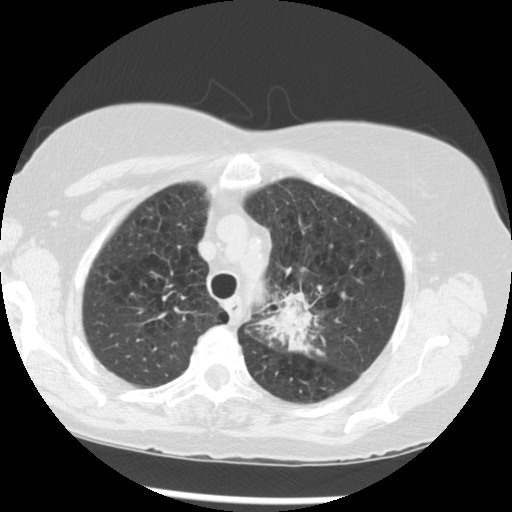
Low-dose screening chest CT, axial slice. Third annual screen. Lung window (W 1500 / L -600 HU). 2.5 mm slice thickness. Standard (soft-tissue) reconstruction kernel (STANDARD). 120 kVp. Female, age 70 years at enrolment. Current smoker at enrolment.
Expert reader's lesion annotation, bounding box <259,275,355,364> (left, top, right, bottom; pixels). Screening reader's record for this exam (one nodule recorded; not confirmed to be the boxed lesion): non-calcified nodule or mass ≥4 mm, left upper lobe, 32 × 26 mm, spiculated (stellate) margins, soft tissue attenuation, pre-existing on the prior screen: yes; interval growth: yes. Participant outcome: lung cancer diagnosed 24 days after this screen — neoplasm, malignant, left upper lobe, stage IIIB (AJCC 6th edition), 40 mm at pathology.